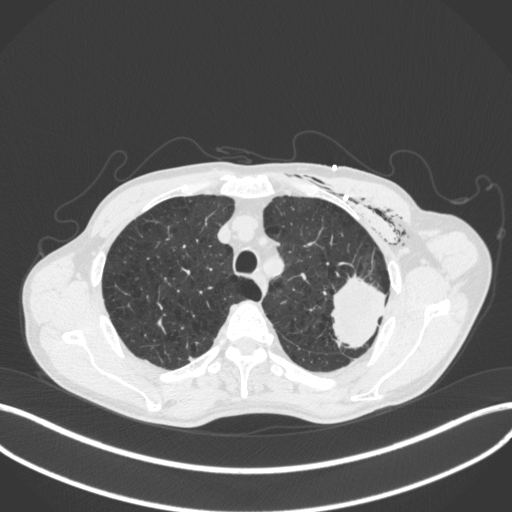
Chest CT, one axial slice. Position 322 of 416 along the scan axis. Reconstruction kernel B31f. 120 kVp. Lung window (W 1500 / L -600 HU). 1 mm slice thickness. 512 × 512 image matrix, field of view 400 × 400 mm. Patient: male, 58 years. Case-level facts recorded for this patient, not image findings: clinical TNM (as recorded): T3 N0 M0.
Outlined on this slice (rectangle marked by the reading radiologist):
- lung tumour (recorded histology: adenocarcinoma): box from (x=324, y=272) to (x=390, y=351) px